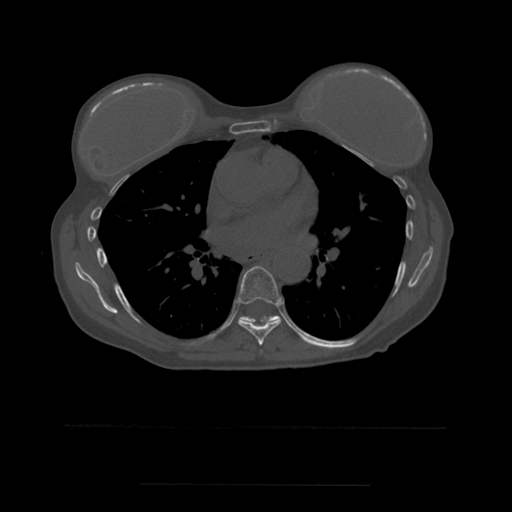
CT including the spine, one axial slice. Bone window (W 1800 / L 400 HU). 1.25 mm slice thickness. 512 × 512 image matrix. Patient age 58 years. Case-level facts recorded for this patient, not image findings: primary cancer: lung.
Structures marked on this image (semi-automatically segmented with operator editing):
- T7 vertebra: bounding box (x1, y1, x2, y2) in pixels: (238, 266, 282, 346)
- T8 vertebra: (239, 316, 281, 323)